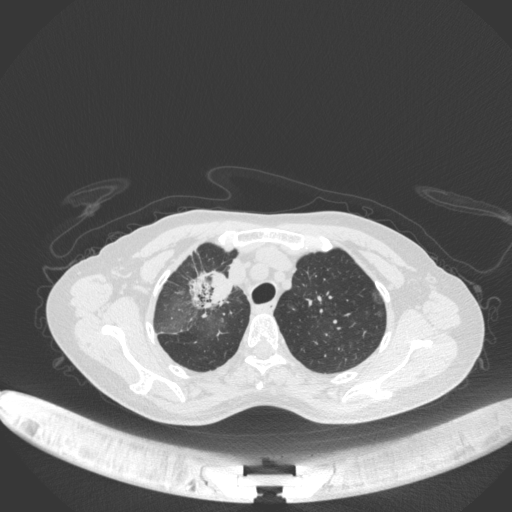
Chest CT, one axial slice. Position 257 of 311 along the scan axis. Reconstruction kernel B31f. Lung window (W 1500 / L -600 HU). 1 mm slice thickness. 512 × 512 image matrix. Female patient, age 59 years. Case-level facts recorded for this patient, not image findings: clinical TNM (as recorded): T3 N0 M0; histopathological grade: G1.
Annotated regions visible in this slice (rectangle marked by the reading radiologist):
- lung tumour (recorded histology: adenocarcinoma): bounding box (x1, y1, x2, y2) in pixels: (186, 269, 233, 316)